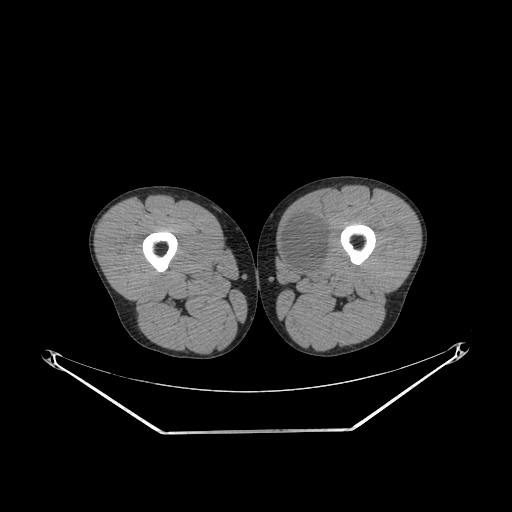
CT of an extremity soft-tissue mass (from a PET/CT study), one axial slice. Position 245 of 311 along the scan axis. 140 kVp. Soft-tissue window (W 400 / L 40 HU). 3.75 mm slice thickness. 512 × 512 image matrix, field of view 500 × 500 mm. Male patient. From the clinical record (not read from this slice): histological type: mixoid liposarcoma; grade: low; site of the primary tumour: left thigh.
Outlined on this slice (expert contour drawn on MRI and transferred to this co-registered scan by the dataset authors):
- gross tumour volume (mass): box from (x=279, y=215) to (x=330, y=275) px